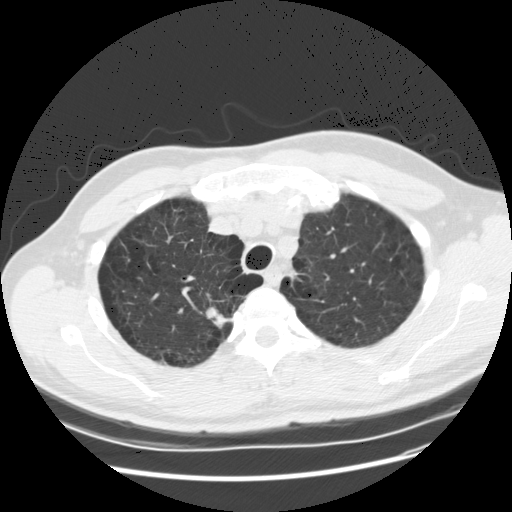
Low-dose screening chest CT, axial slice; baseline annual screen; lung window (W 1500 / L -600 HU); standard (soft-tissue) reconstruction kernel (STANDARD); 120 kVp; slice 28 of 132 in the series; 512 × 512 image matrix. Male, age 61 years at enrolment. Former smoker at enrolment.
• Expert-annotated lung lesion, bounding box <190,289,240,340> (left, top, right, bottom; pixels).
• The exam's reader record, not a measurement of the box and not confirmed to be the same lesion: non-calcified nodule or mass ≥4 mm, right upper lobe, 19 × 13 mm, poorly defined margins, soft tissue attenuation.
• Participant outcome: lung cancer diagnosed 62 days after this screen — squamous cell carcinoma, NOS, right upper lobe, poorly differentiated (G3), stage IA (AJCC 6th edition), 20 mm at pathology.